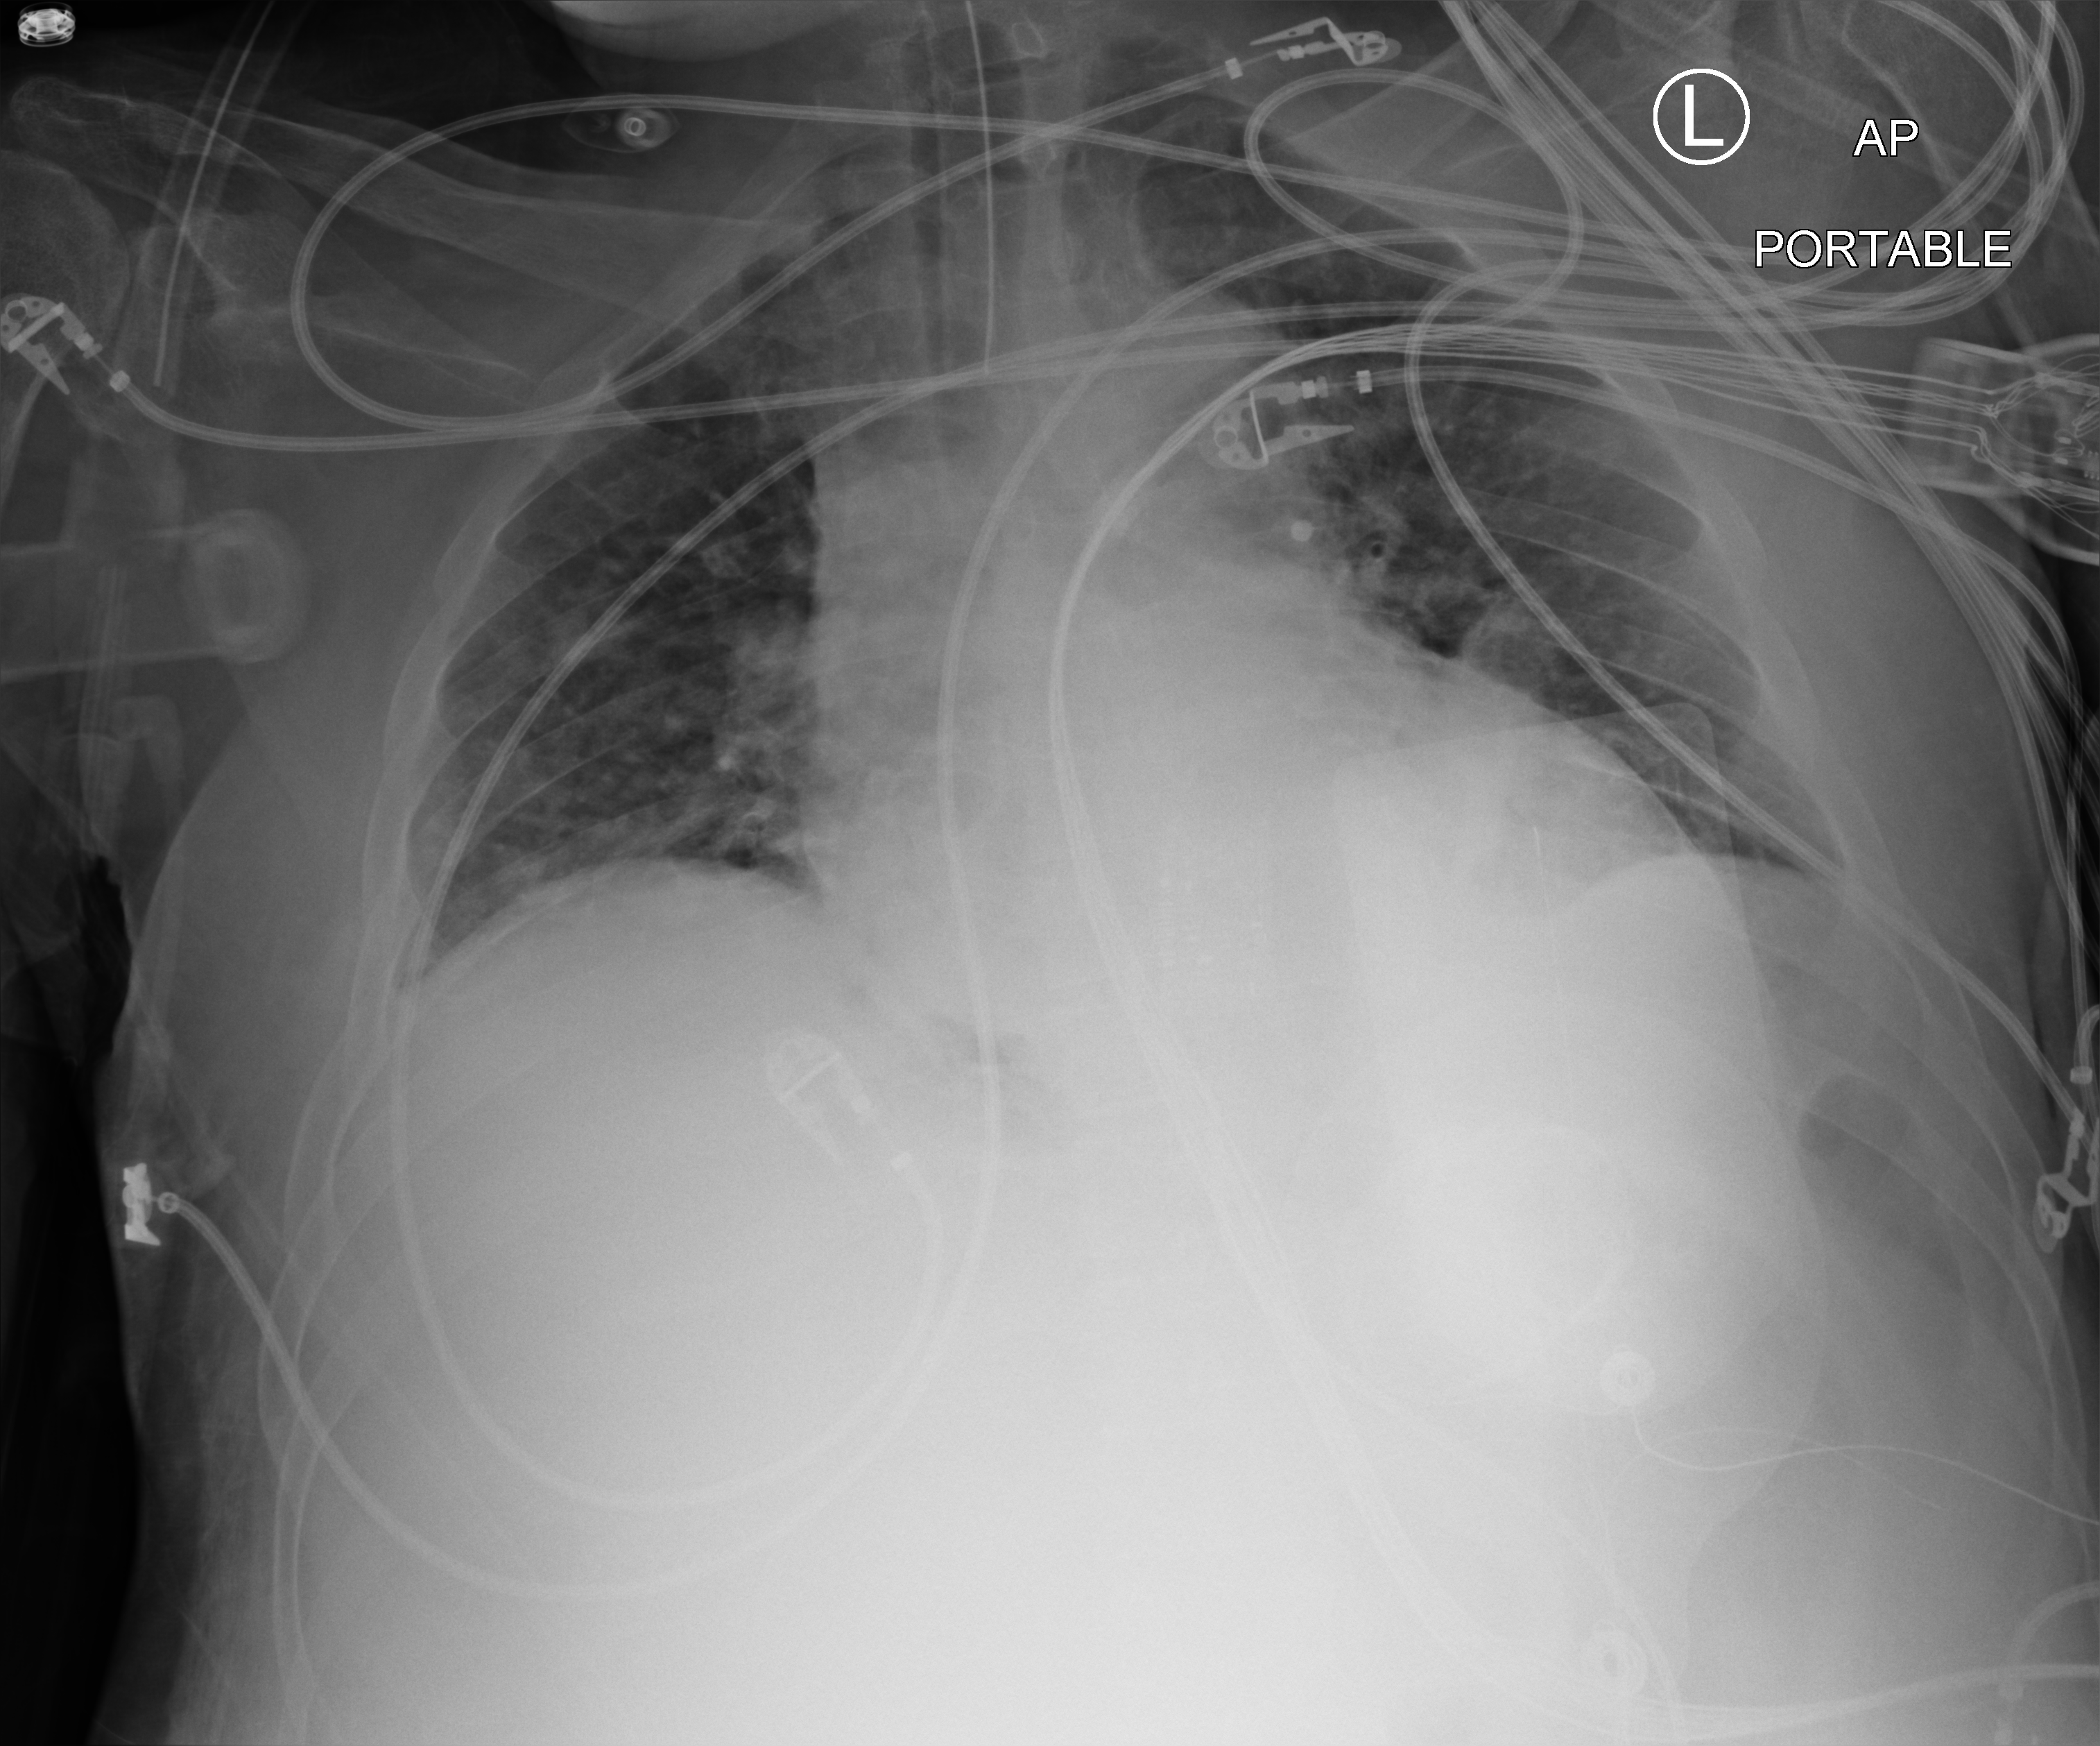
Portable chest radiograph, anteroposterior (AP) projection. Male patient hospitalised with COVID-19, age 60–74 years.
From the hospital-stay record, not from the radiograph (when in the stay this image was taken is not recorded): mechanically ventilated during this hospital stay: yes; COPD (admission record): no.